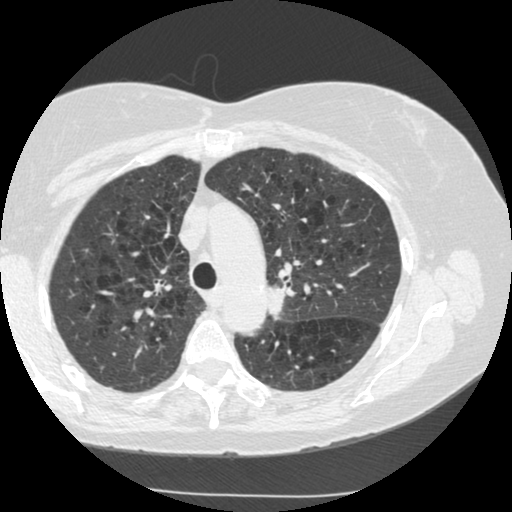
Chest CT (low-dose screening protocol), one axial image. Second screening round (one year after baseline). Lung window (W 1500 / L -600 HU). 120 kVp. Slice 188 of 249 in the series. Female, age 70 years at enrolment. Current smoker at enrolment.
• Expert reader's lesion annotation, bounding box [x1, y1, x2, y2] px = [246, 268, 313, 330].
• Reader record for this screening exam (exam-level; its link to the box is not recorded): non-calcified nodule or mass ≥4 mm, left upper lobe, 15 × 13 mm, spiculated (stellate) margins, soft tissue attenuation, pre-existing on the prior screen: yes; interval growth: yes.
• Official screen result: positive, other.
• Participant outcome: lung cancer diagnosed 360 days after this screen (after the third annual screen) — neoplasm, malignant, left upper lobe, stage IIIB (AJCC 6th edition), 40 mm at pathology.